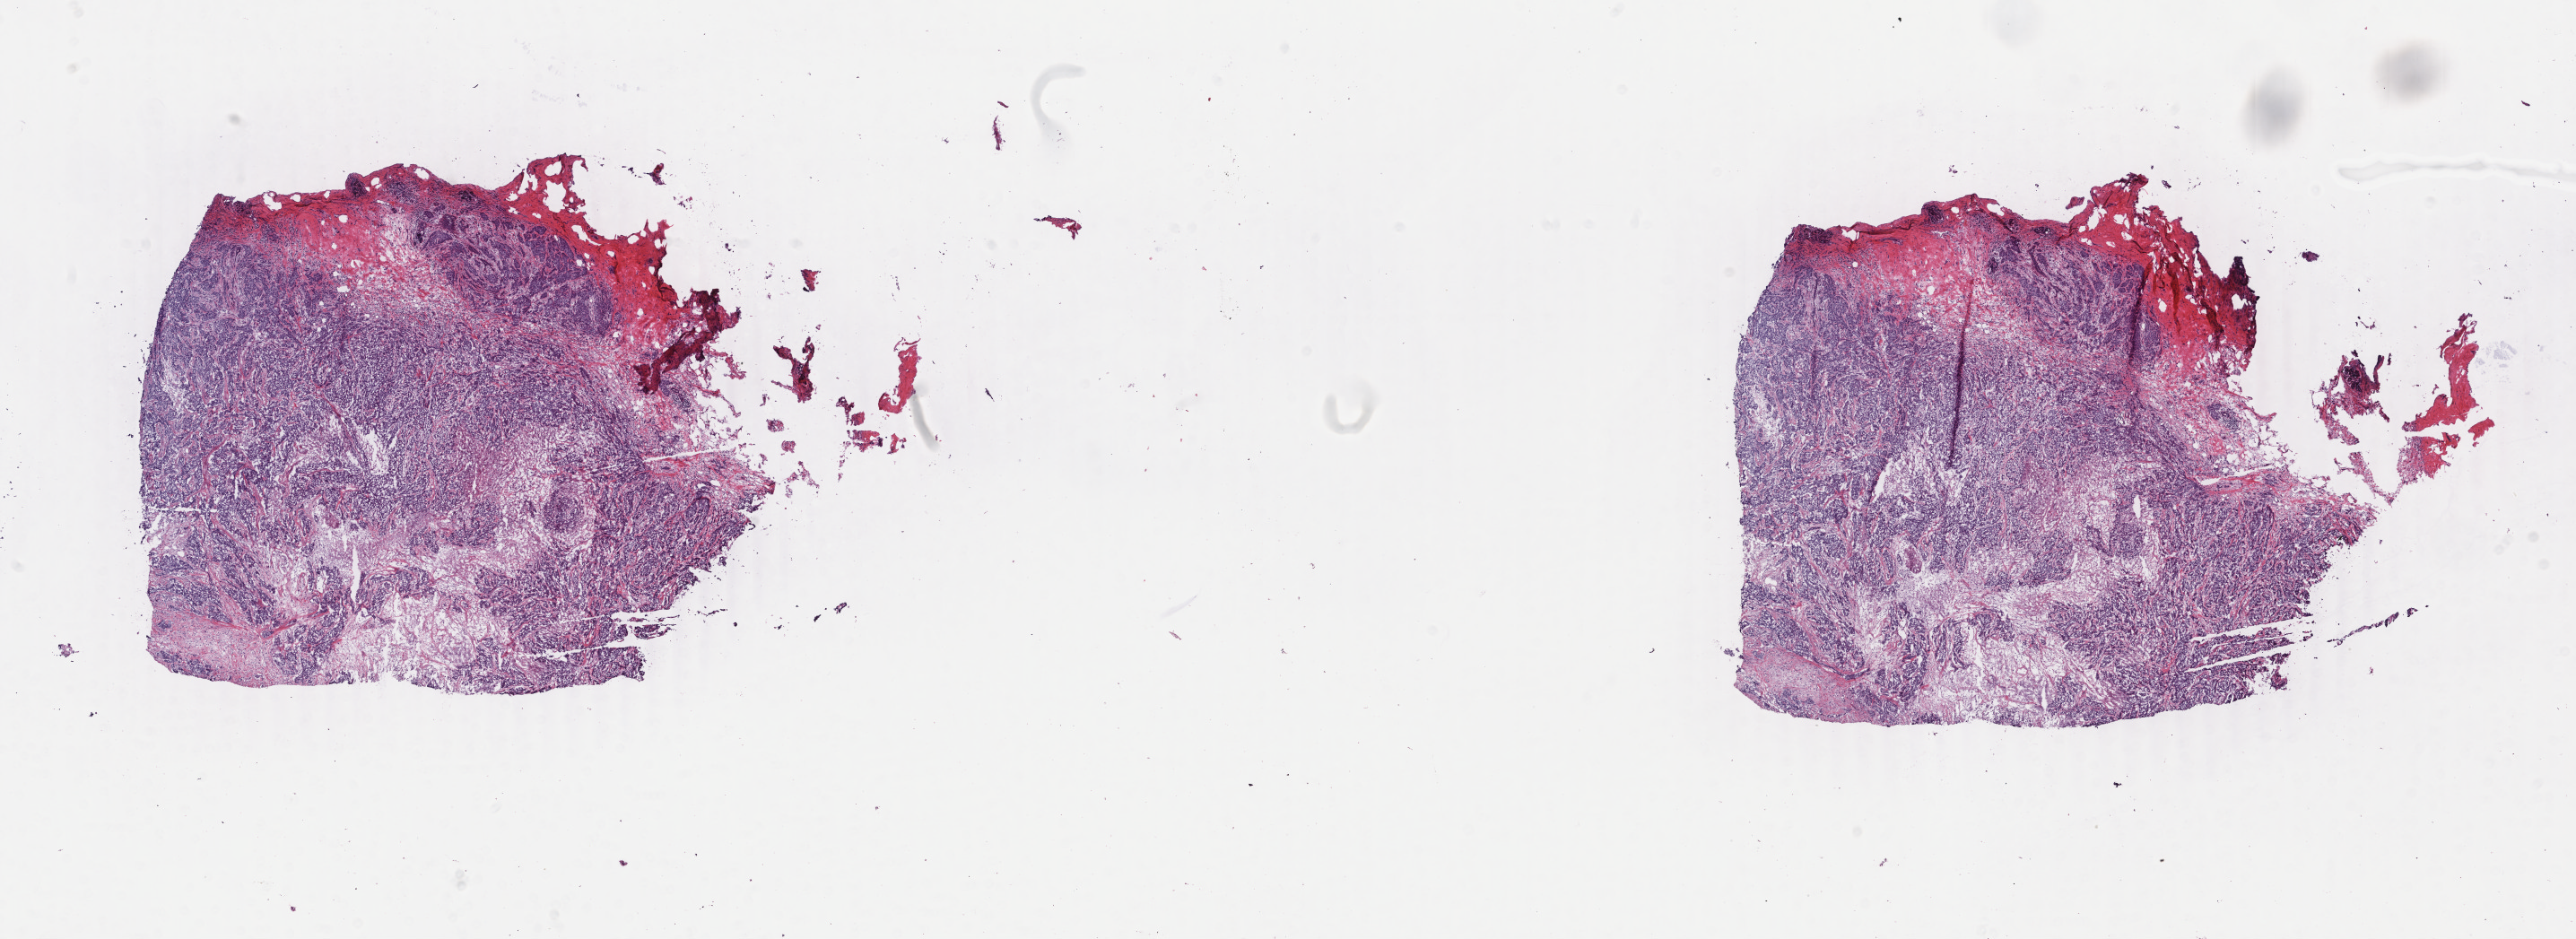
Digitized Hematoxylin and eosin (H&E) stained tissue section (whole slide) — low-resolution overview of the scanned area, about 22.8 x 8.3 mm, frozen section, primary tumour sample from the breast. Patient: female, age at initial diagnosis 65 years.
Histologic diagnosis: Infiltrating duct carcinoma, NOS.